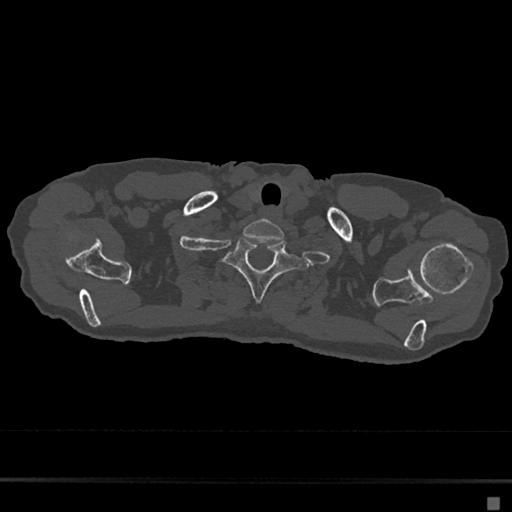
CT including the spine, one axial slice; slice 610 of 797 in the series (ordered by position); reconstruction kernel Br40s/3; bone window (W 1800 / L 400 HU); 0.5 mm slice thickness; 512 × 512 image matrix, field of view 360 × 360 mm. Patient: female, 68 years. Case-level facts recorded for this patient, not image findings: primary cancer: renal.
Structures marked on this image (semi-automatically segmented with operator editing):
- T1 vertebra: box from (x=224, y=237) to (x=302, y=302) px
- T2 vertebra: (x=216, y=279)–(x=220, y=284)